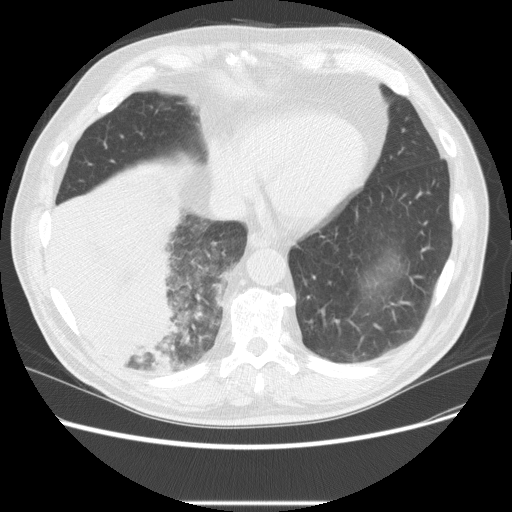
Low-dose screening chest CT, one axial slice. Position 64 of 233 along the scan axis. Reconstruction kernel STANDARD. Lung window (W 1500 / L -600 HU). 512 × 512 image matrix, field of view 380 × 380 mm.
Outlined on this slice (outlined manually by an expert reader):
- lesion 3 (tumor, lower lobe of right lung): box from (x=48, y=194) to (x=181, y=367) px